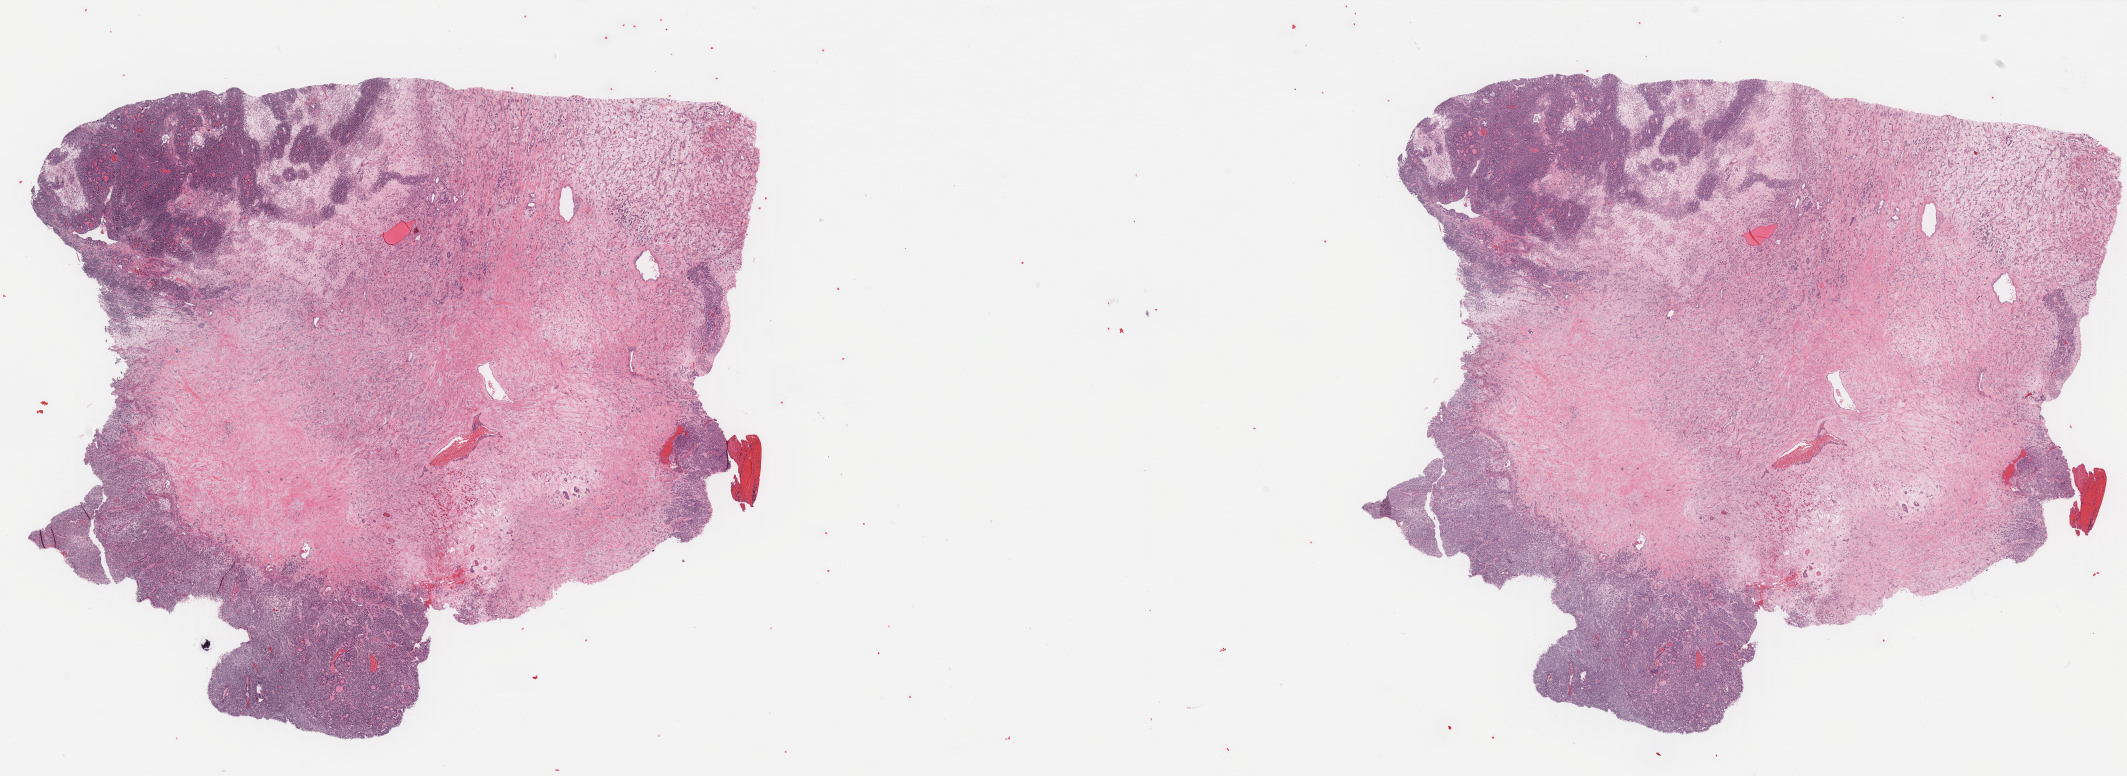
H&E-stained whole-slide image — whole scanned area (about 33.7 x 12.3 mm, from a 40x scan) shown as a low-resolution overview; formalin-fixed paraffin-embedded (FFPE) diagnostic section; sample: primary tumour, thyroid. Male, age 28 years at initial diagnosis.
- TNM: T2 NX M0
- pathologic diagnosis: Papillary adenocarcinoma, NOS (thyroid gland)
- AJCC pathologic stage: I (7th edition)